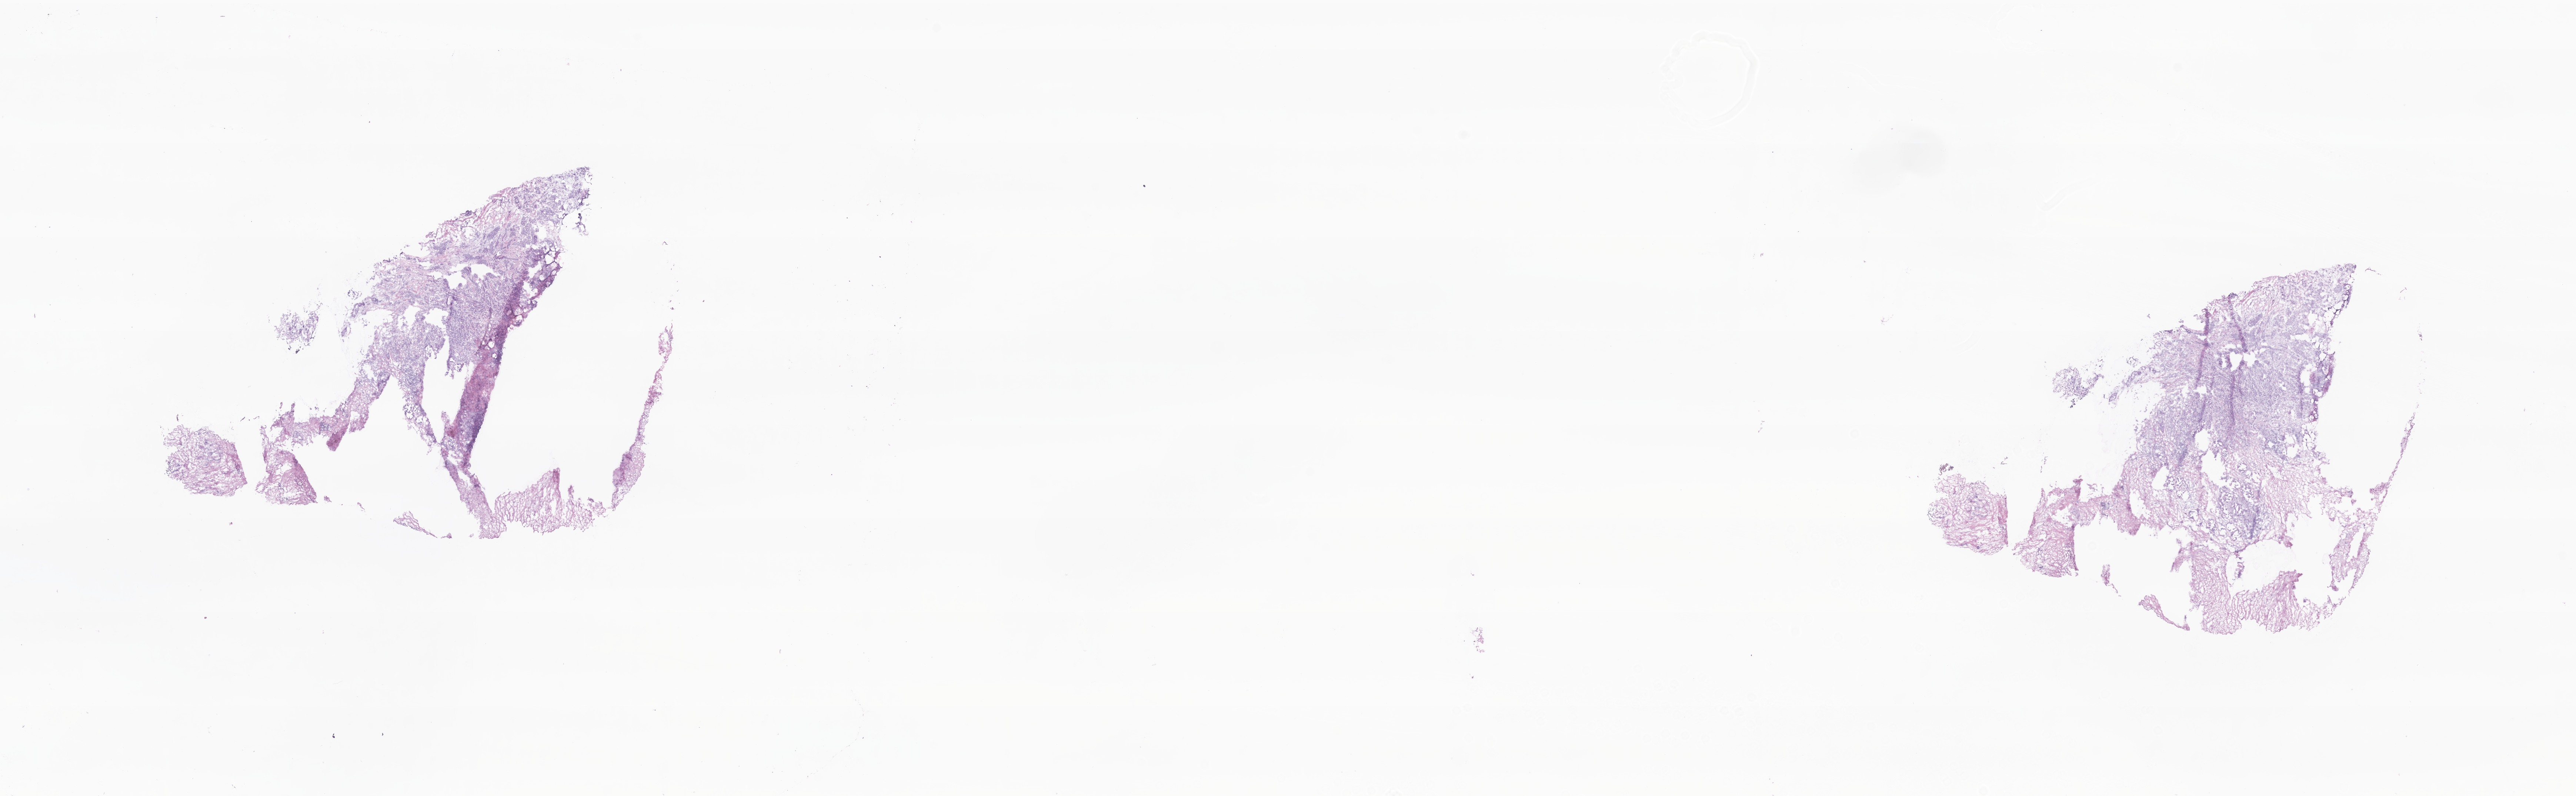
Digitized haematoxylin and eosin-stained section, a low-resolution overview of the entire scanned area, about 29.3 x 9.1 mm. Cryosection. Primary tumor. Site: breast (right). Female, age 60 years at initial diagnosis. Slide review estimates, as recorded: tumor cells 35%, tumor nuclei 90%, stromal cells 65%, necrosis 0%, normal cells 0%. Inflammatory infiltration, as recorded: lymphocyte infiltration 4%, monocyte infiltration 0%, neutrophil infiltration 0%.
Diagnosis: Infiltrating duct carcinoma, NOS.